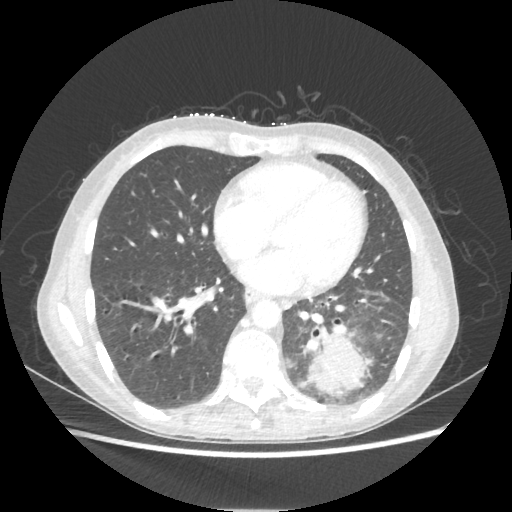
Chest CT, one axial slice. Slice 88 of 221 in the series (ordered by position). Reconstruction kernel STANDARD. 80 kVp. Lung window (W 1500 / L -600 HU). 1.25 mm slice thickness. 512 × 512 image matrix. Patient: female, 53 years. Case-level facts recorded for this patient, not image findings: clinical TNM (as recorded): T3 N0 M0.
Annotated regions visible in this slice (bounding box drawn by a radiologist):
- lung tumour (recorded histology: adenocarcinoma): bounding box (x1, y1, x2, y2) in pixels: (304, 327, 367, 394)